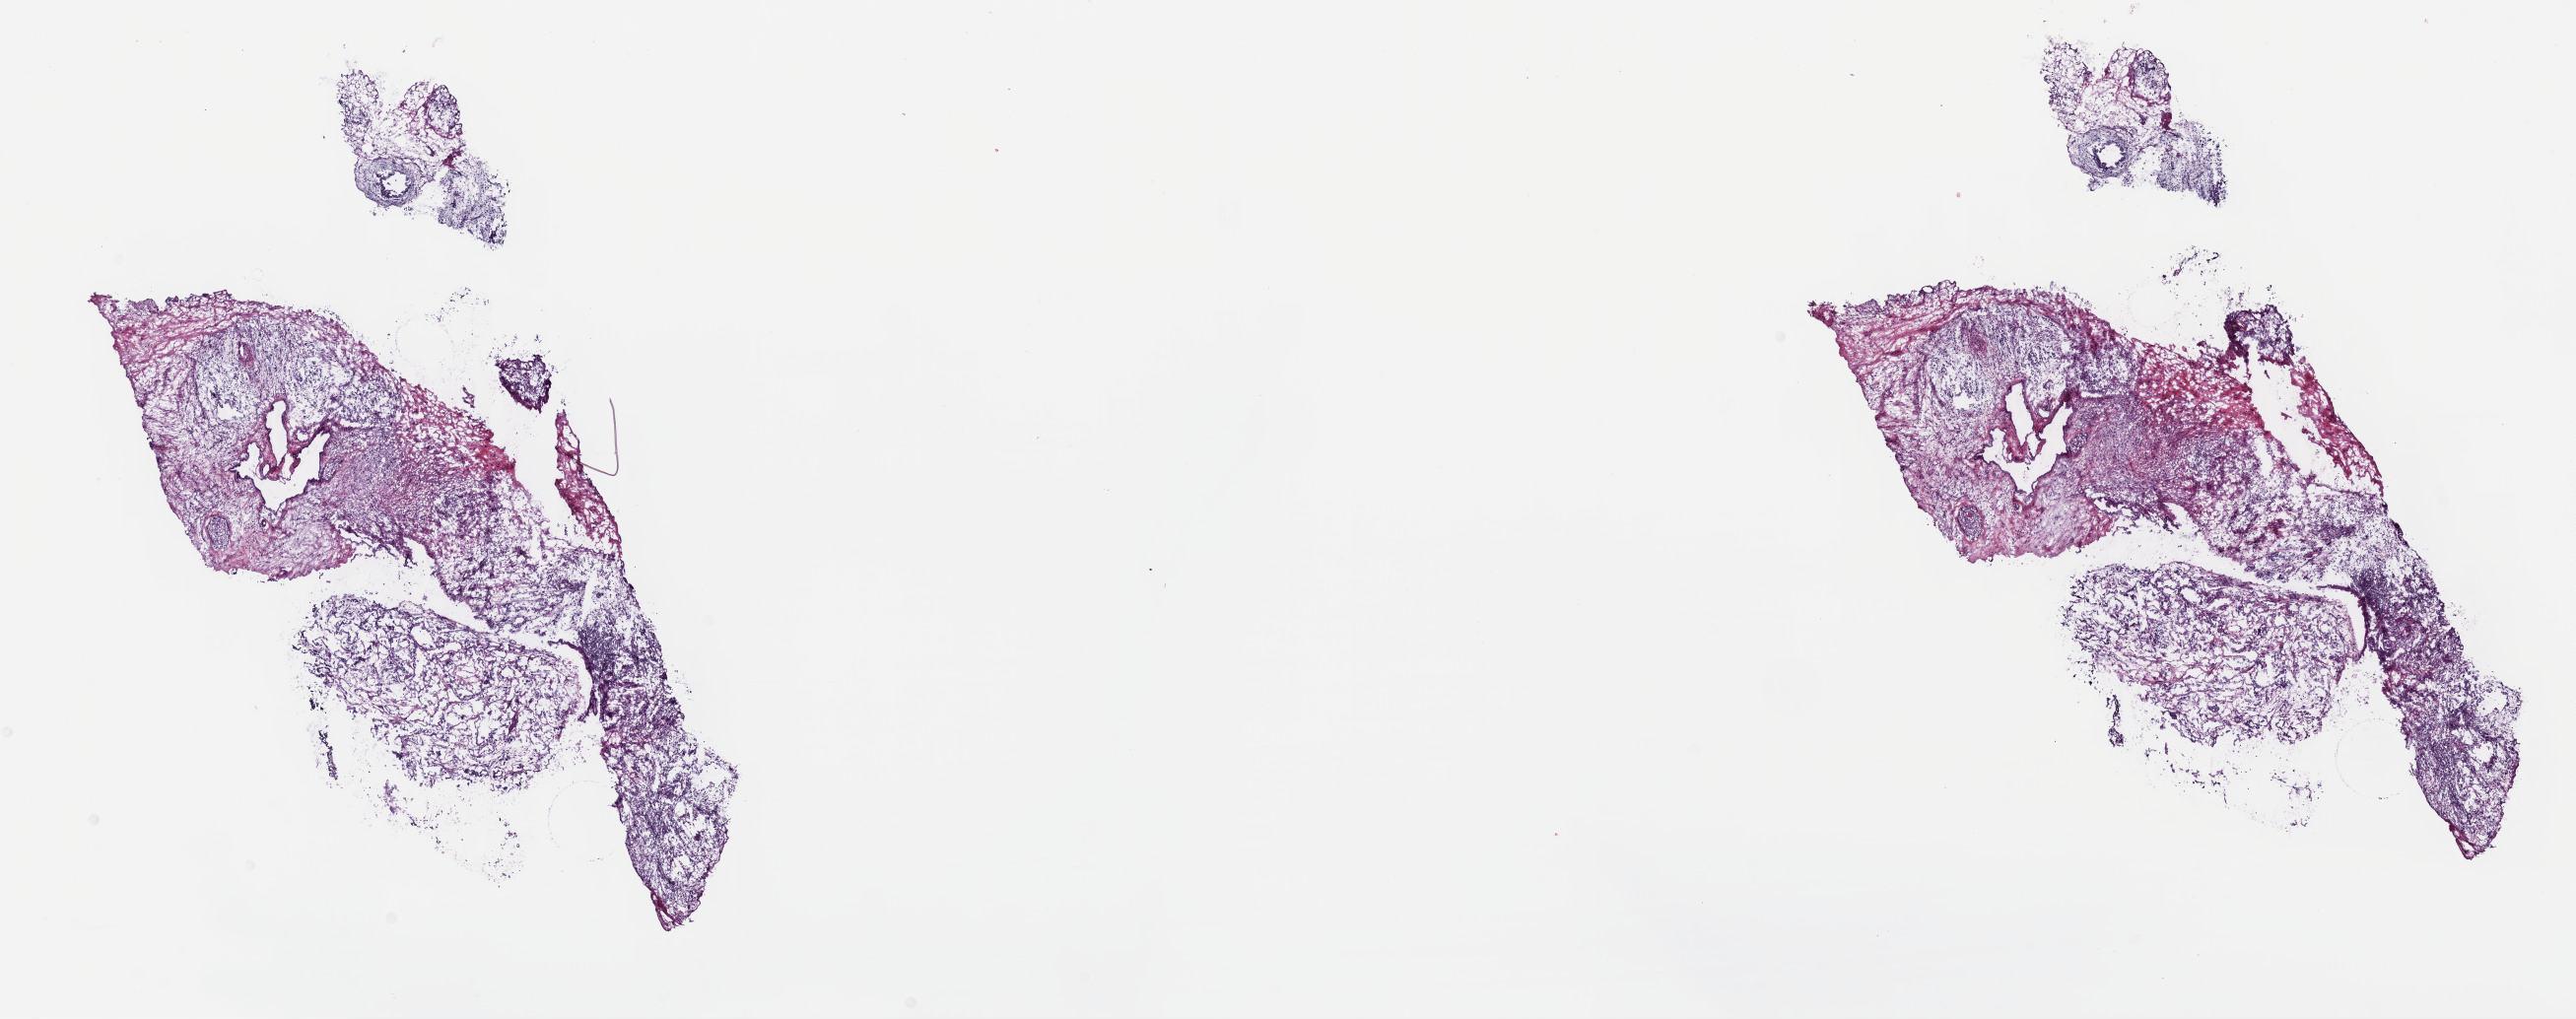
Whole-slide histology image, H&E-stained, a low-resolution overview of the entire scanned area, about 21.1 x 8.4 mm, frozen section from the top of the tissue portion, sample: primary tumour, testis. Male, age 29 years at initial diagnosis. Composition of this section per pathologist review: tumour cells 100%, tumour nuclei 80%, normal cells 0%, stromal cells 0%, necrosis 0%. Inflammatory infiltration, as recorded: lymphocyte infiltration 1%, monocyte infiltration 0%, neutrophil infiltration 0%.
AJCC pathologic stage: IS. Histologic diagnosis: Mixed germ cell tumor. Laterality: left.